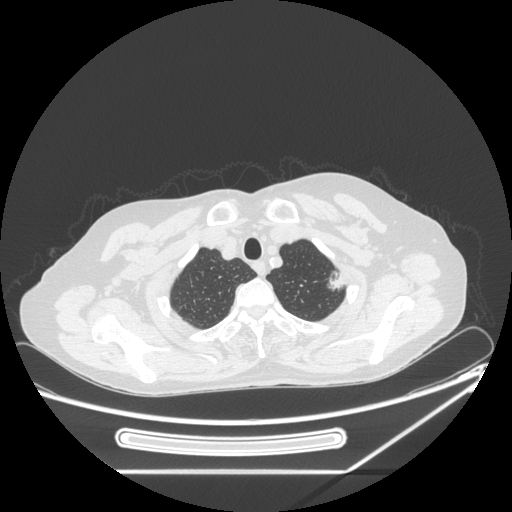
Chest CT, one axial slice; slice 213 of 250 in the series (ordered by position); reconstruction kernel STANDARD; lung window (W 1500 / L -600 HU); 1.25 mm slice thickness; 512 × 512 image matrix, field of view 409 × 409 mm. Patient: female, 57 years. Case-level facts recorded for this patient, not image findings: clinical TNM (as recorded): T1c N0 M0.
Structures marked on this image (bounding box drawn by a radiologist):
- lung tumour (recorded histology: adenocarcinoma): bounding box (x1, y1, x2, y2) in pixels: (322, 261, 348, 295)